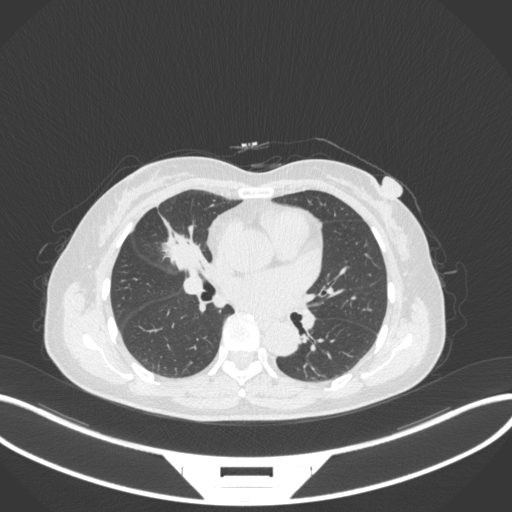
Chest CT, one axial slice; slice 155 of 282 in the series (ordered by position); reconstruction kernel B31f; lung window (W 1500 / L -600 HU); 1 mm slice thickness; 512 × 512 image matrix. Patient: female, 51 years. From the clinical record (not read from this slice): clinical TNM (as recorded): T1c N0 M0; histopathological grade: G2.
Outlined on this slice (bounding box drawn by a radiologist):
- lung tumour (recorded histology: adenocarcinoma): bounding box (x1, y1, x2, y2) in pixels: (151, 215, 208, 272)